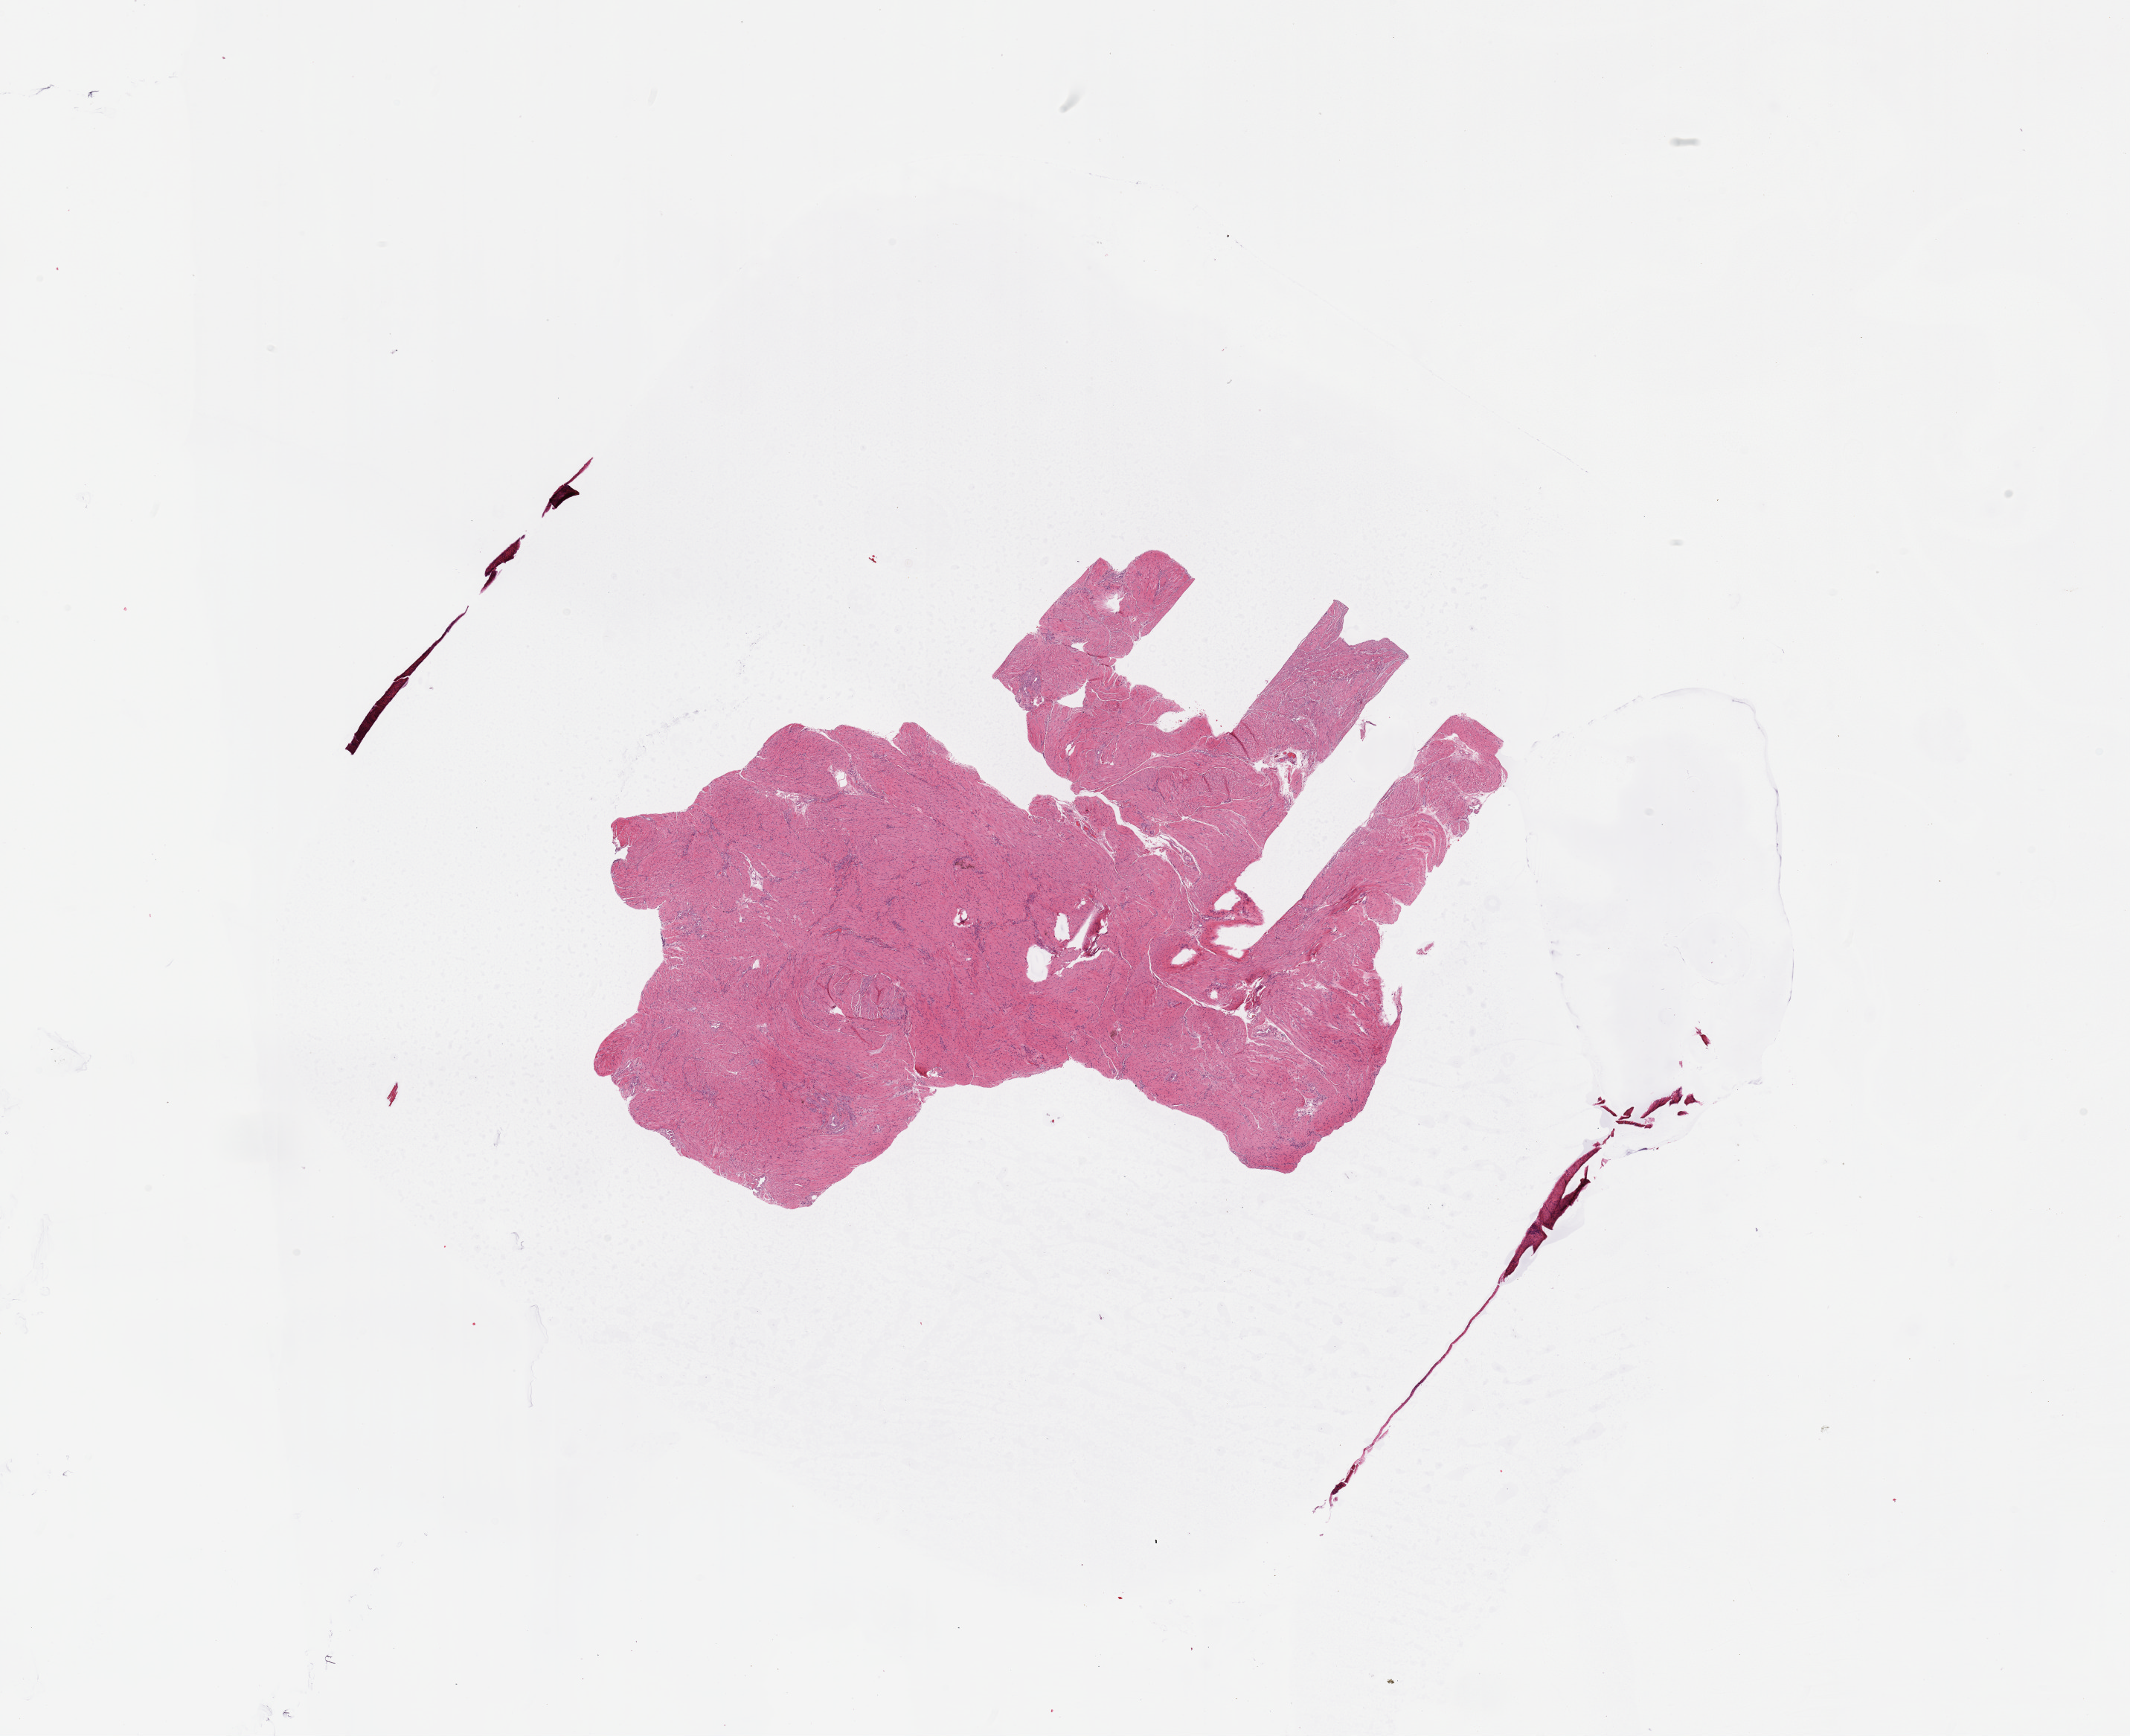
Digitized Hematoxylin and eosin (H&E) stained tissue section (whole slide), a low-resolution overview of the entire scanned area, about 22.6 x 18.5 mm; uterus, normal (non-tumour) tissue. Patient: female, age 46 years.
This section: normal (non-tumour) tissue from the same patient. Patient diagnosis: Endometrioid adenocarcinoma, NOS.